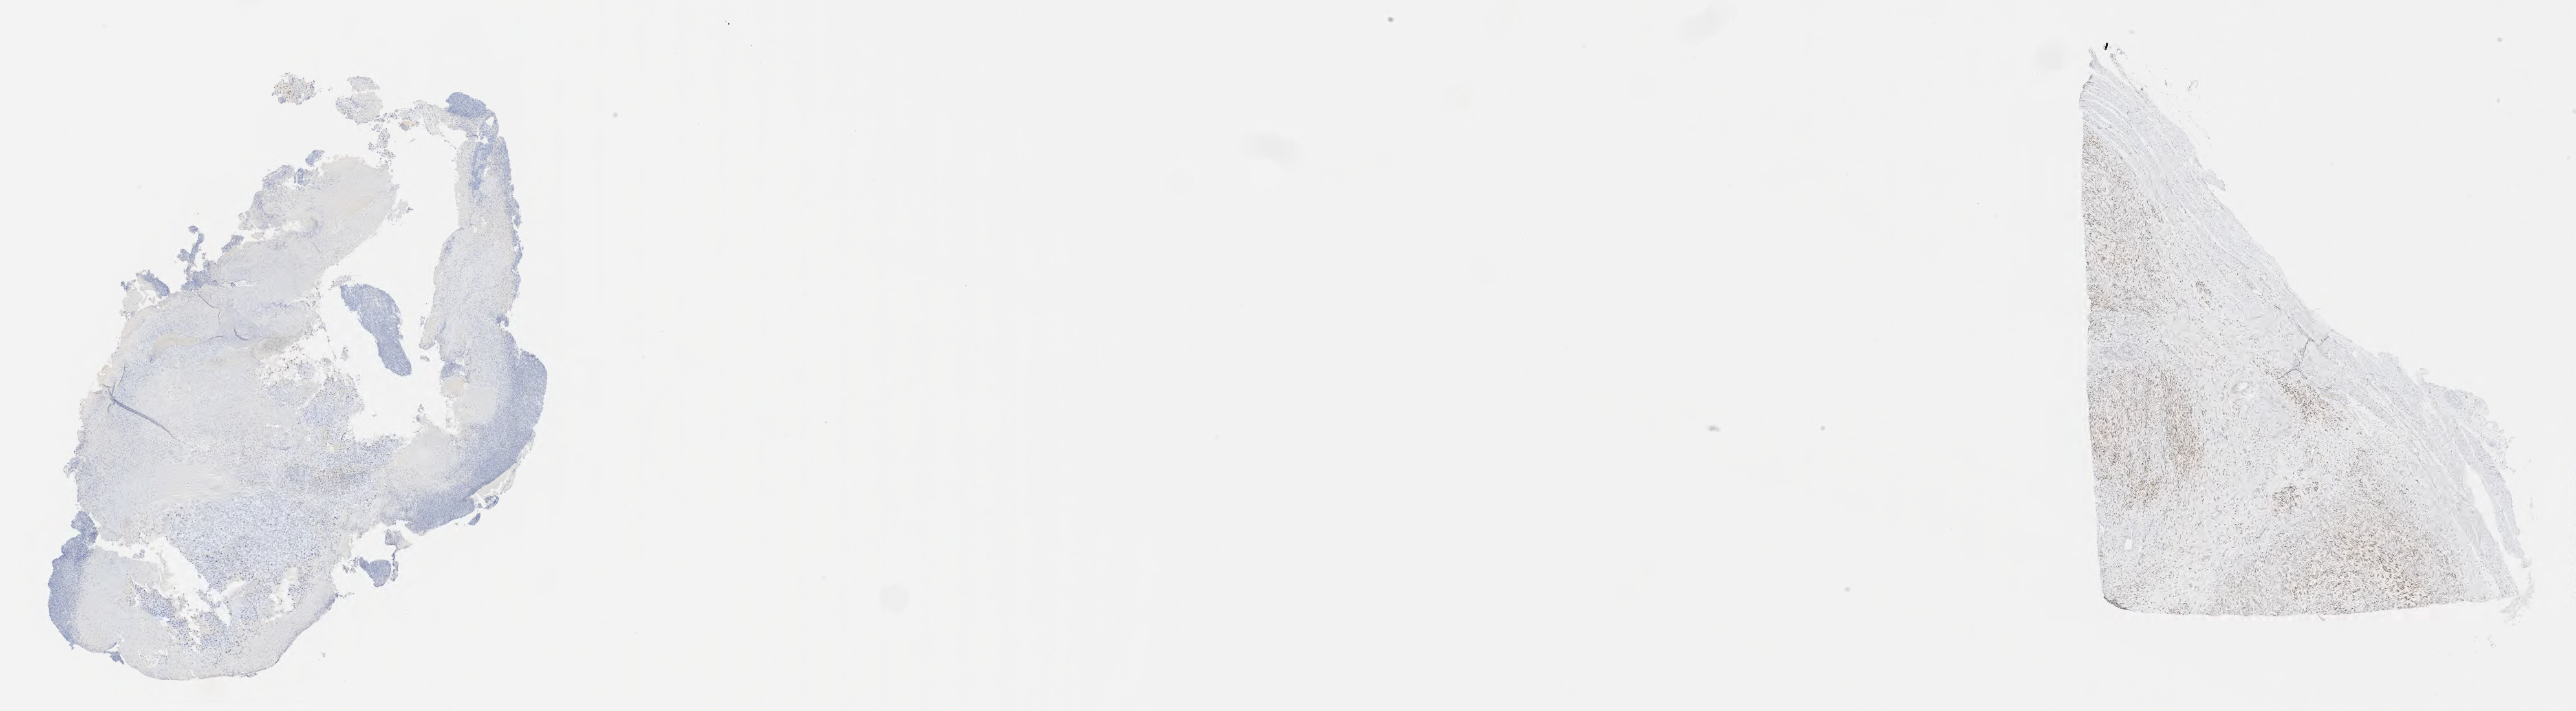
Whole-slide image, immunohistochemical stain for estrogen receptor (ER) — whole scanned area (about 32.2 x 8.9 mm) shown as a low-resolution overview, specimen: tumor tissue, anatomic site: cervix. Female patient, aged 62.
Histologic diagnosis: Squamous cell carcinoma, large cell, nonkeratinizing, NOS.